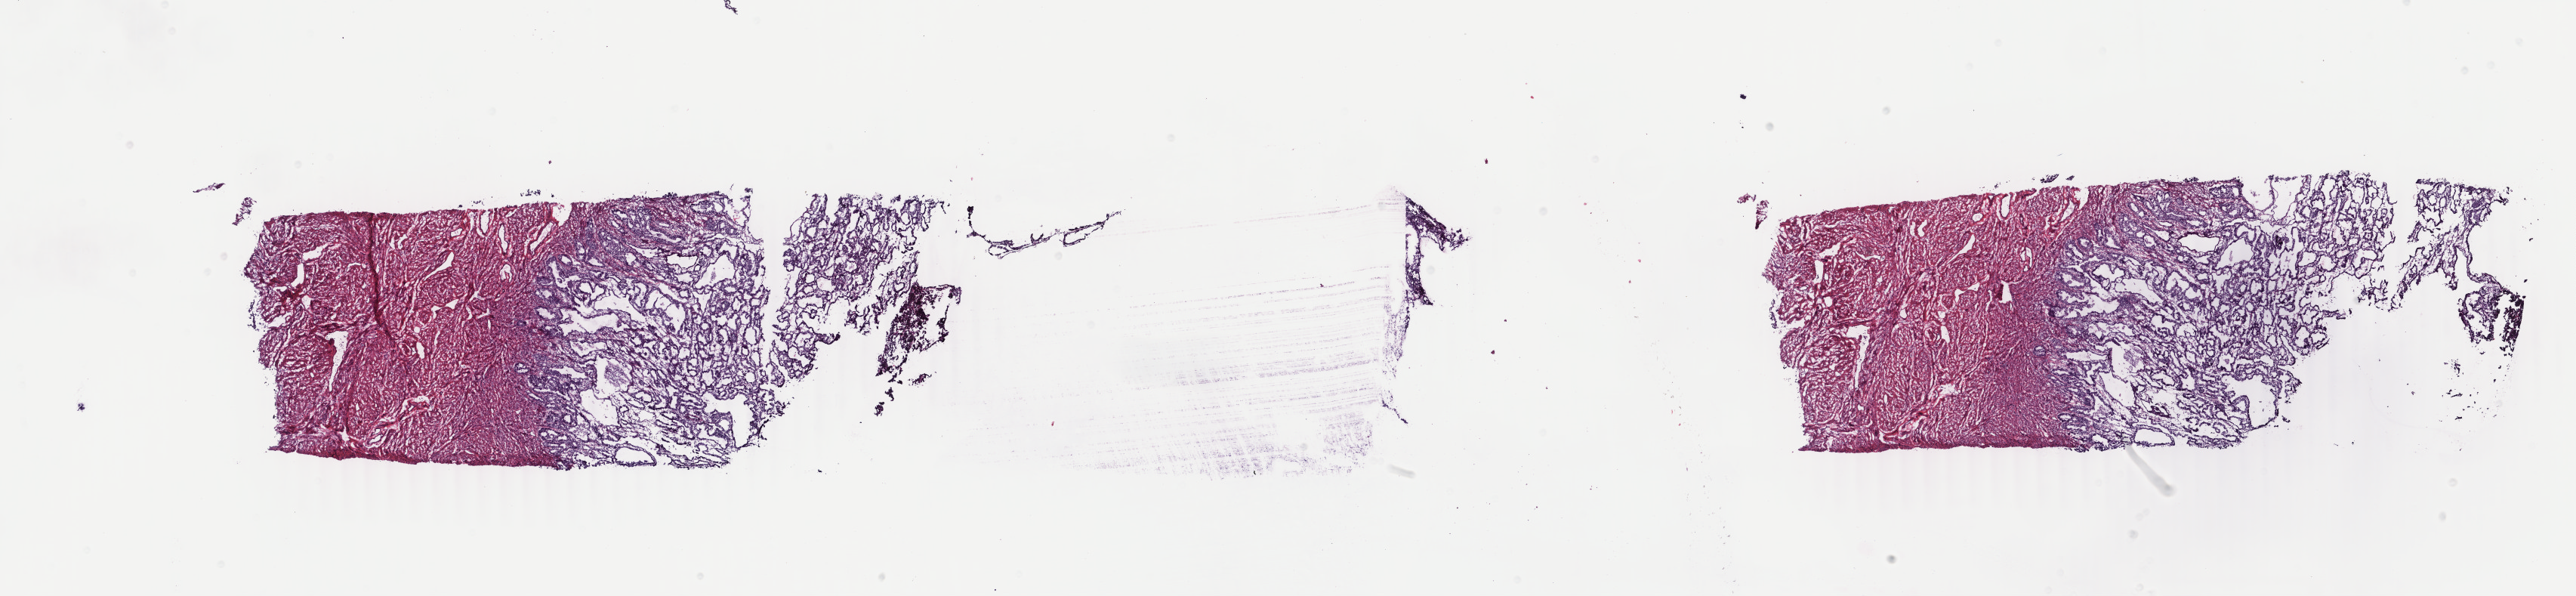
Digitized H&E-stained tissue section (whole slide), a low-resolution overview of the entire scanned area, about 27.1 x 6.3 mm. Frozen section from the top of the tissue portion. Uterus, primary tumour sample. Patient: female, age at initial diagnosis 63 years. Histologic grade: G1 (well differentiated). Slide review estimates, as recorded: tumour cells 50%, tumour nuclei 40%, normal cells 50%, stromal cells 0%, necrosis 0%. Inflammatory infiltration, as recorded: lymphocyte infiltration 0%, monocyte infiltration 0%, neutrophil infiltration 0%.
* diagnosis: Endometrioid adenocarcinoma, NOS (endometrium)
* FIGO stage: IIIA